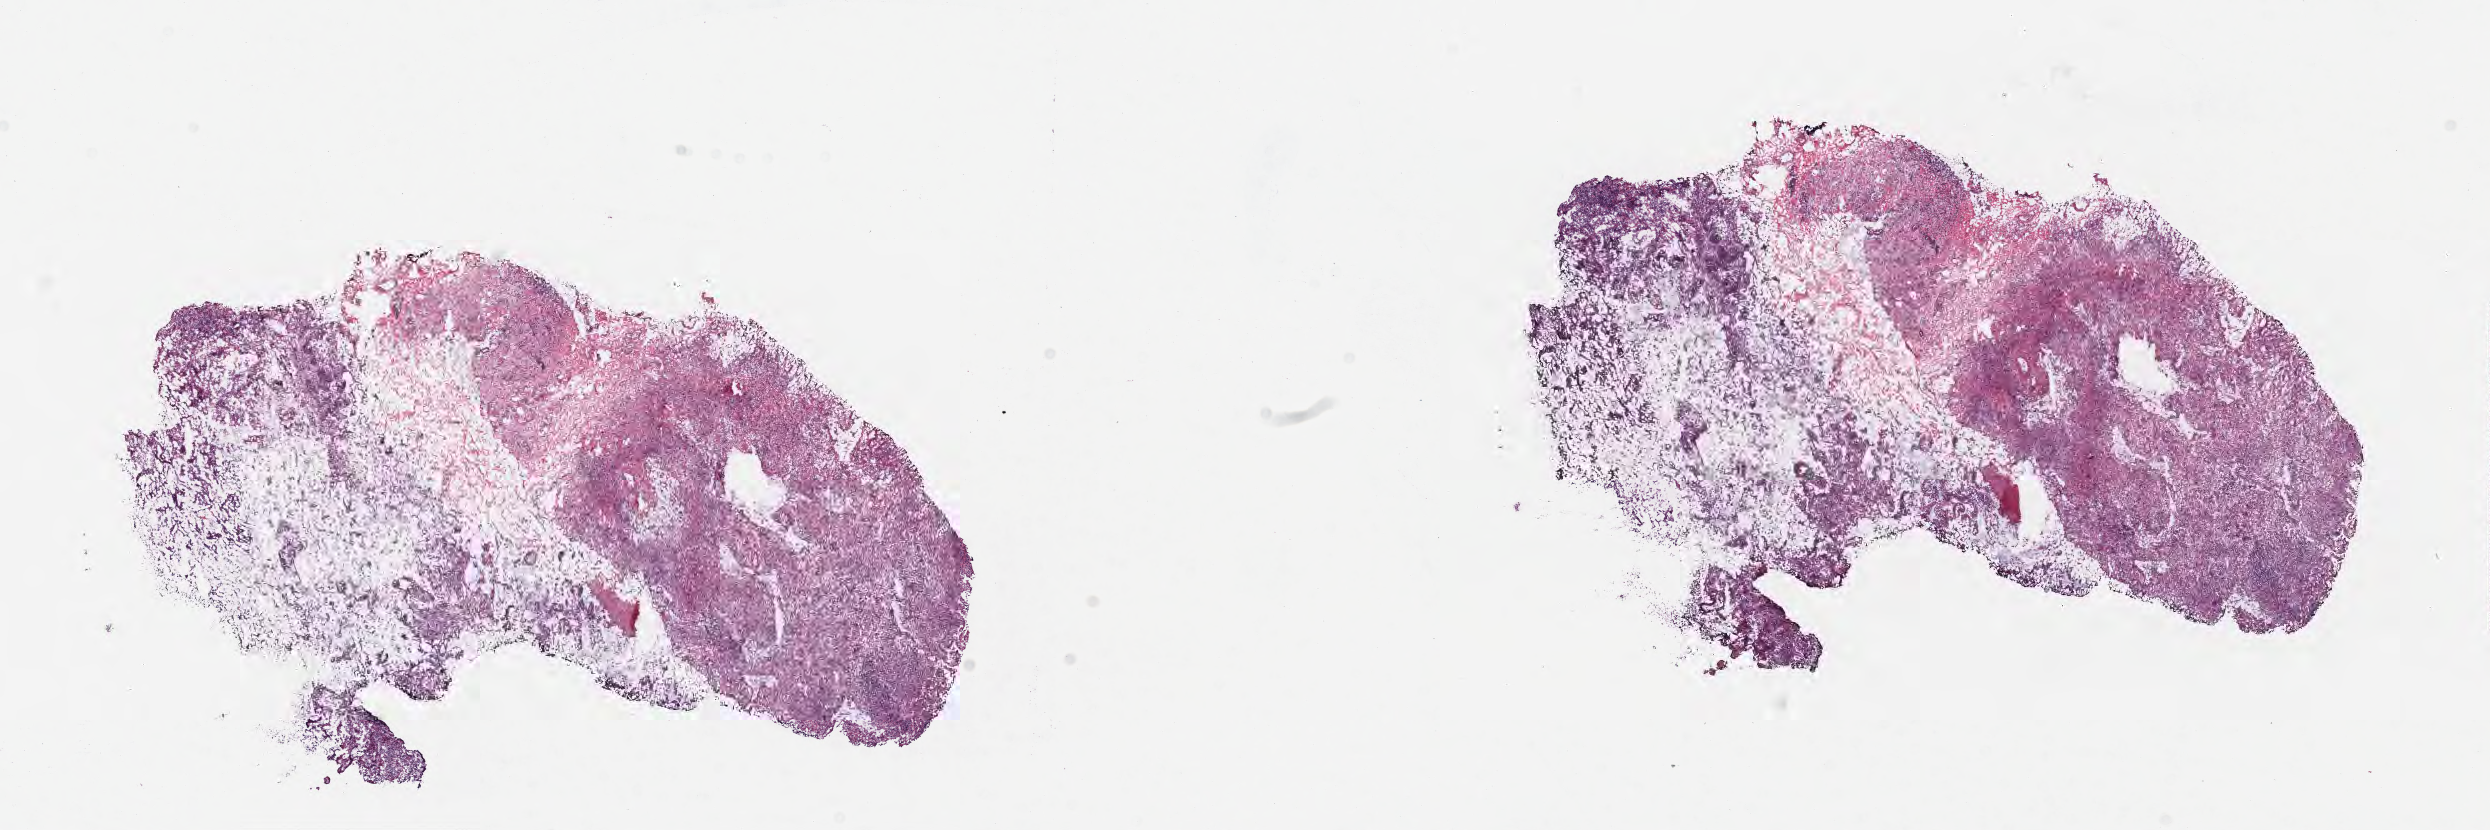
Digitized haematoxylin and eosin-stained section — a low-resolution overview of the entire scanned area, about 20.1 x 6.7 mm; frozen section (tissue freezing medium); specimen: primary tumor; anatomic site: rectosigmoid junction. Male patient; age at initial diagnosis 62 years. Pathologist review of this section (percent, as recorded): tumor cells 77%, tumor nuclei 80%.
Histologic diagnosis: Adenocarcinoma, NOS.